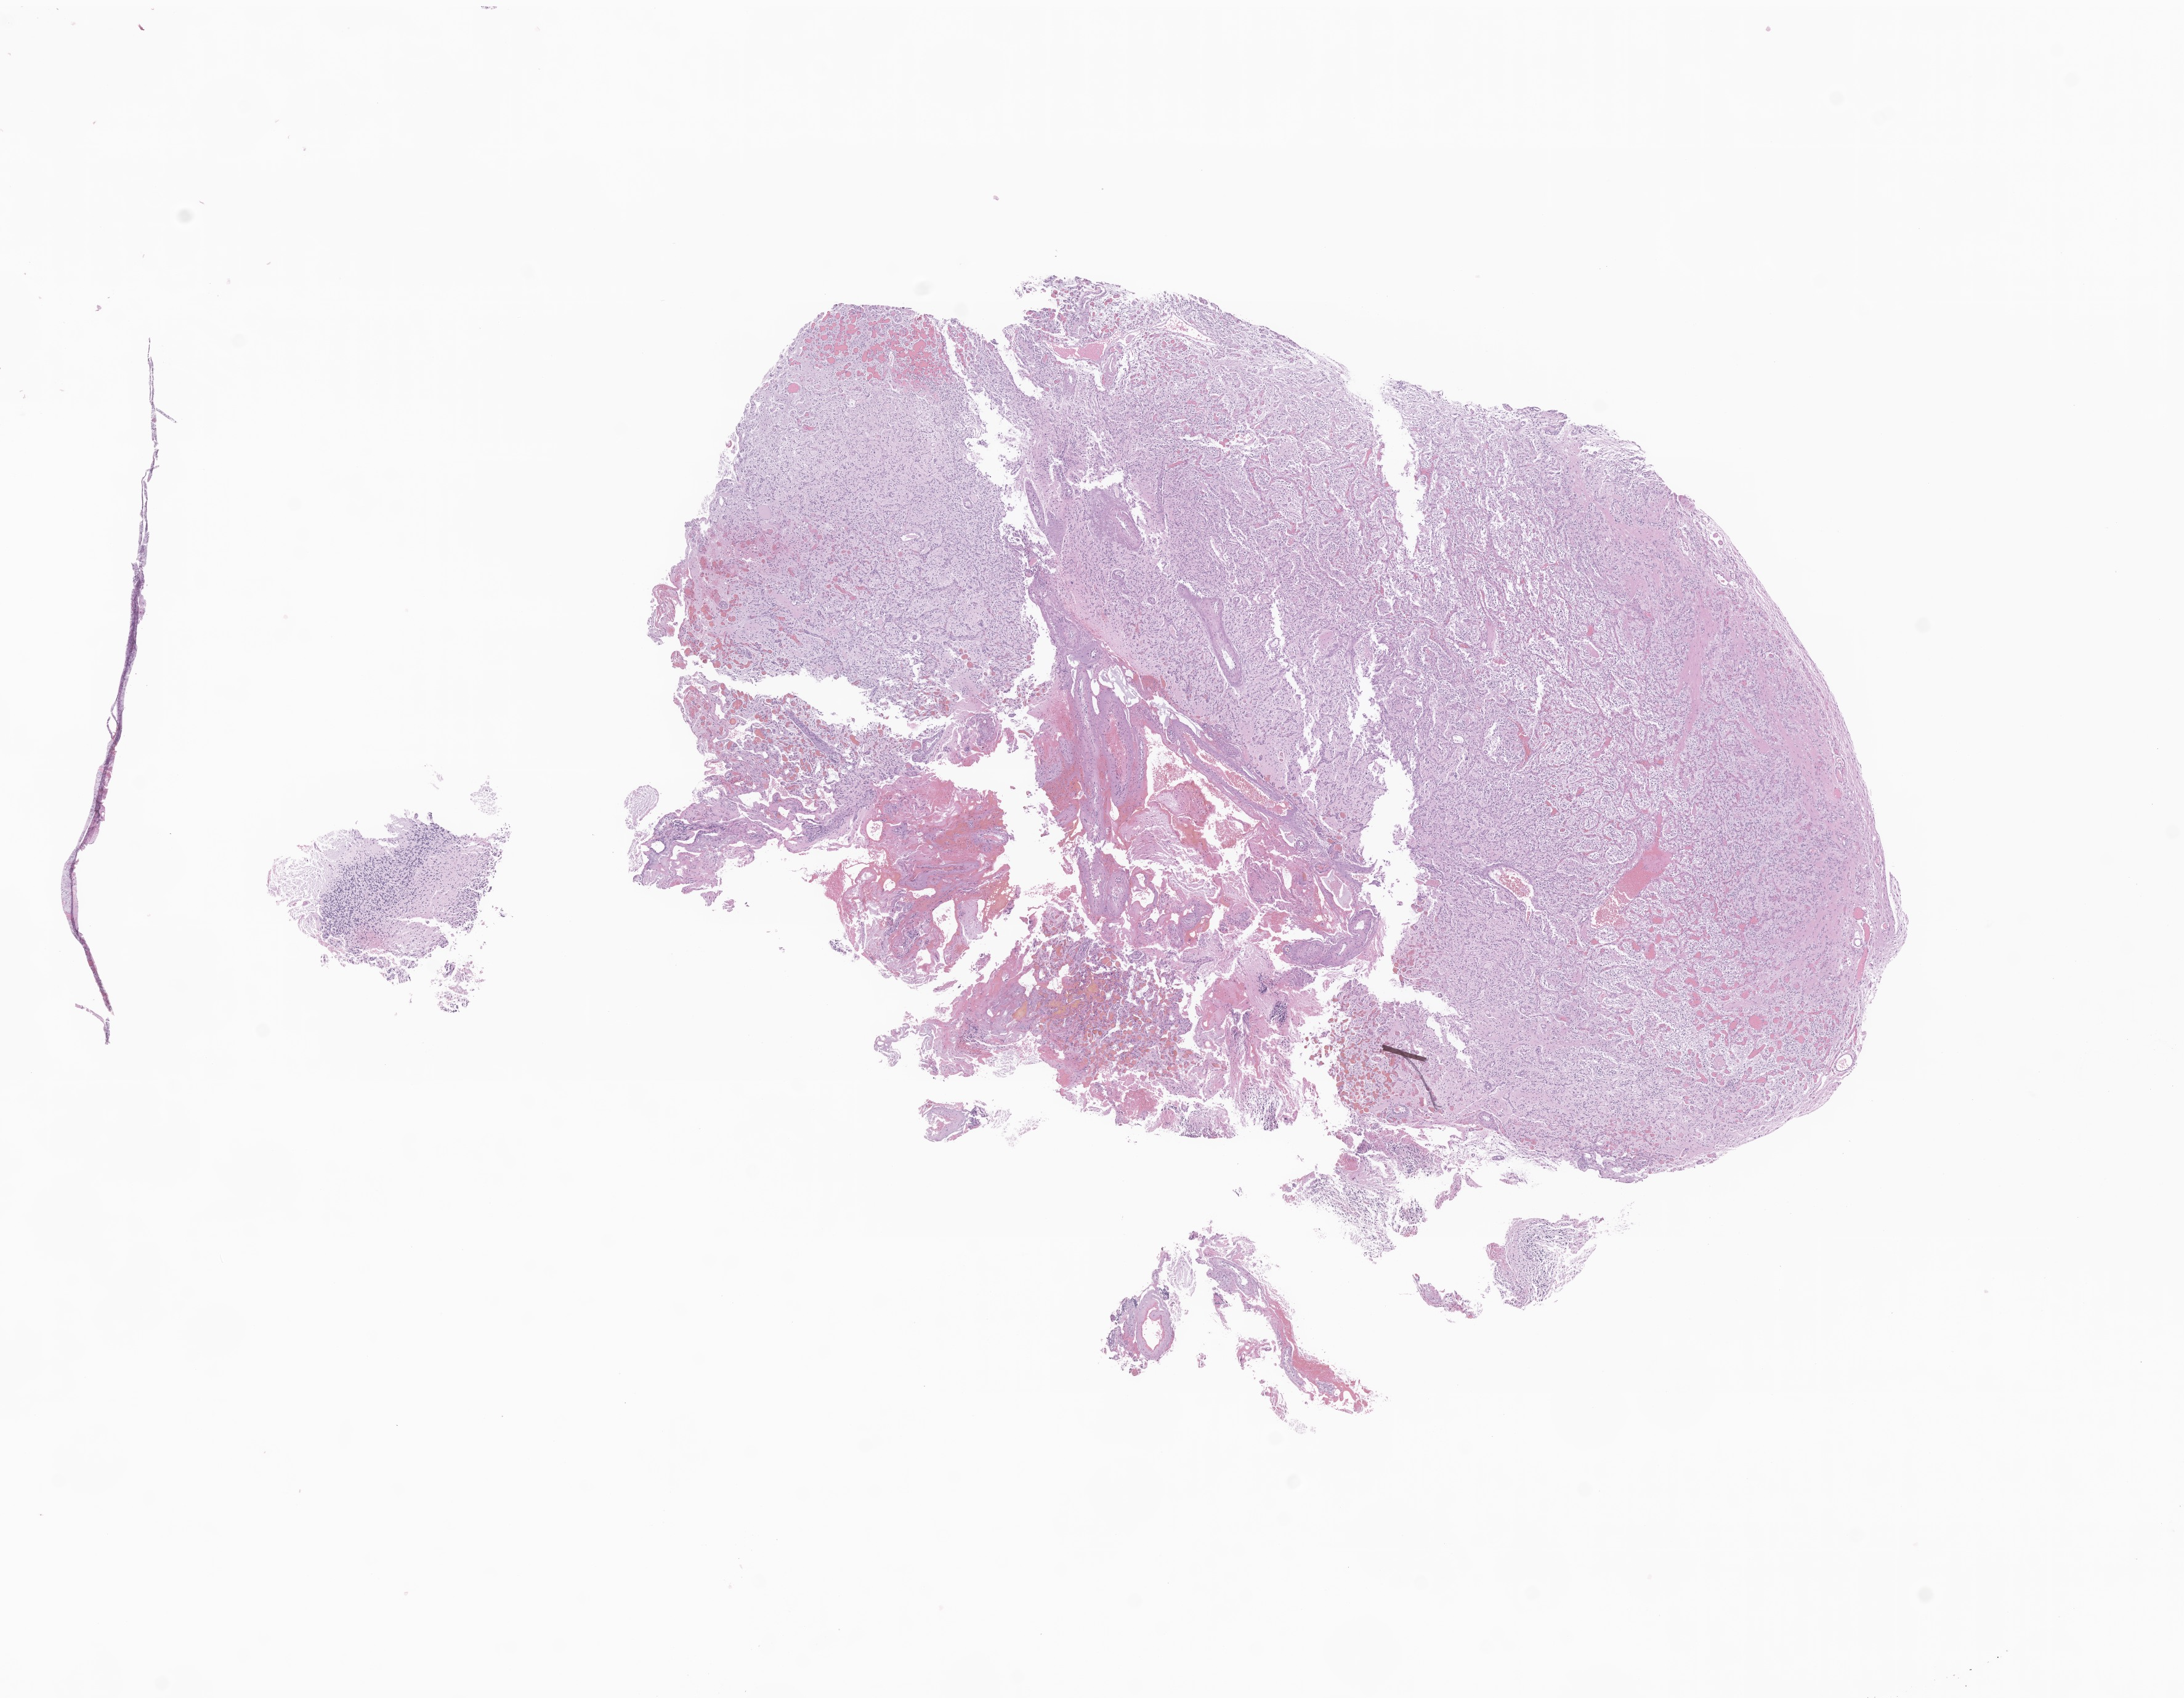
Digitized haematoxylin and eosin-stained section of tumor tissue from the brain — shown as a low-resolution overview of the whole scanned area (about 14.9 x 11.6 mm), formalin-fixed paraffin-embedded section. Patient: male, age 230 months.
Diagnosis: Hemangioblastoma.